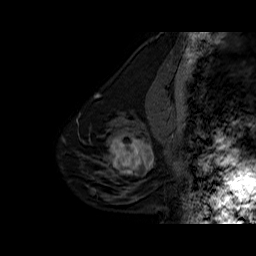
Breast MRI (dynamic contrast-enhanced), one sagittal slice. Position 18 of 60 along the scan axis. Dynamic contrast-enhanced series, time point 2 of 6 at this slice position (early post-contrast). 1.5 T. TE 6.3 ms, TR 32.5 ms. 4 mm slice thickness. 256 × 256 image matrix, field of view 200 × 200 mm. Female patient. Case-level facts recorded for this patient, not image findings: setting: breast cancer imaged before/during neoadjuvant chemotherapy; receptor status: triple-negative.
Structures marked on this image (semi-automatically segmented with operator editing):
- analysis volume of interest (the breast-tissue region the enhancement analysis was run in; not a lesion): bounding box <102,127,162,186> (left, top, right, bottom; pixels)
- tumour enhancement mask (voxels above the 100 % enhancement threshold inside the analysis volume of interest): <109,136,154,175>